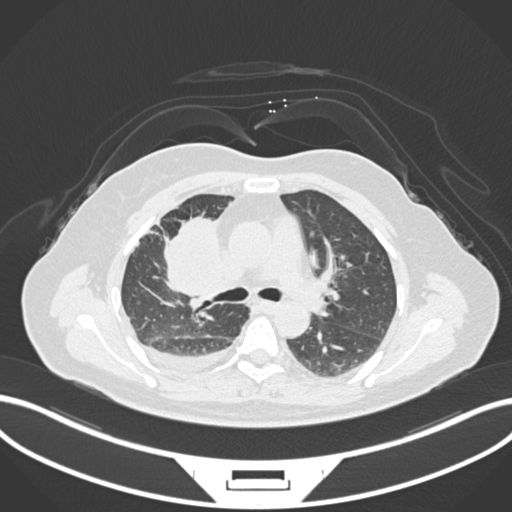
Chest CT, one axial slice; slice 93 of 172 in the series (ordered by position); reconstruction kernel B30f; 120 kVp; lung window (W 1500 / L -600 HU); 512 × 512 image matrix, field of view 400 × 400 mm. Patient: female, 52 years. Case-level facts recorded for this patient, not image findings: clinical TNM (as recorded): T3 N1 M1.
Structures marked on this image (bounding box drawn by a radiologist):
- lung tumour (recorded histology: adenocarcinoma): bounding box [x1, y1, x2, y2] px = [156, 213, 225, 307]